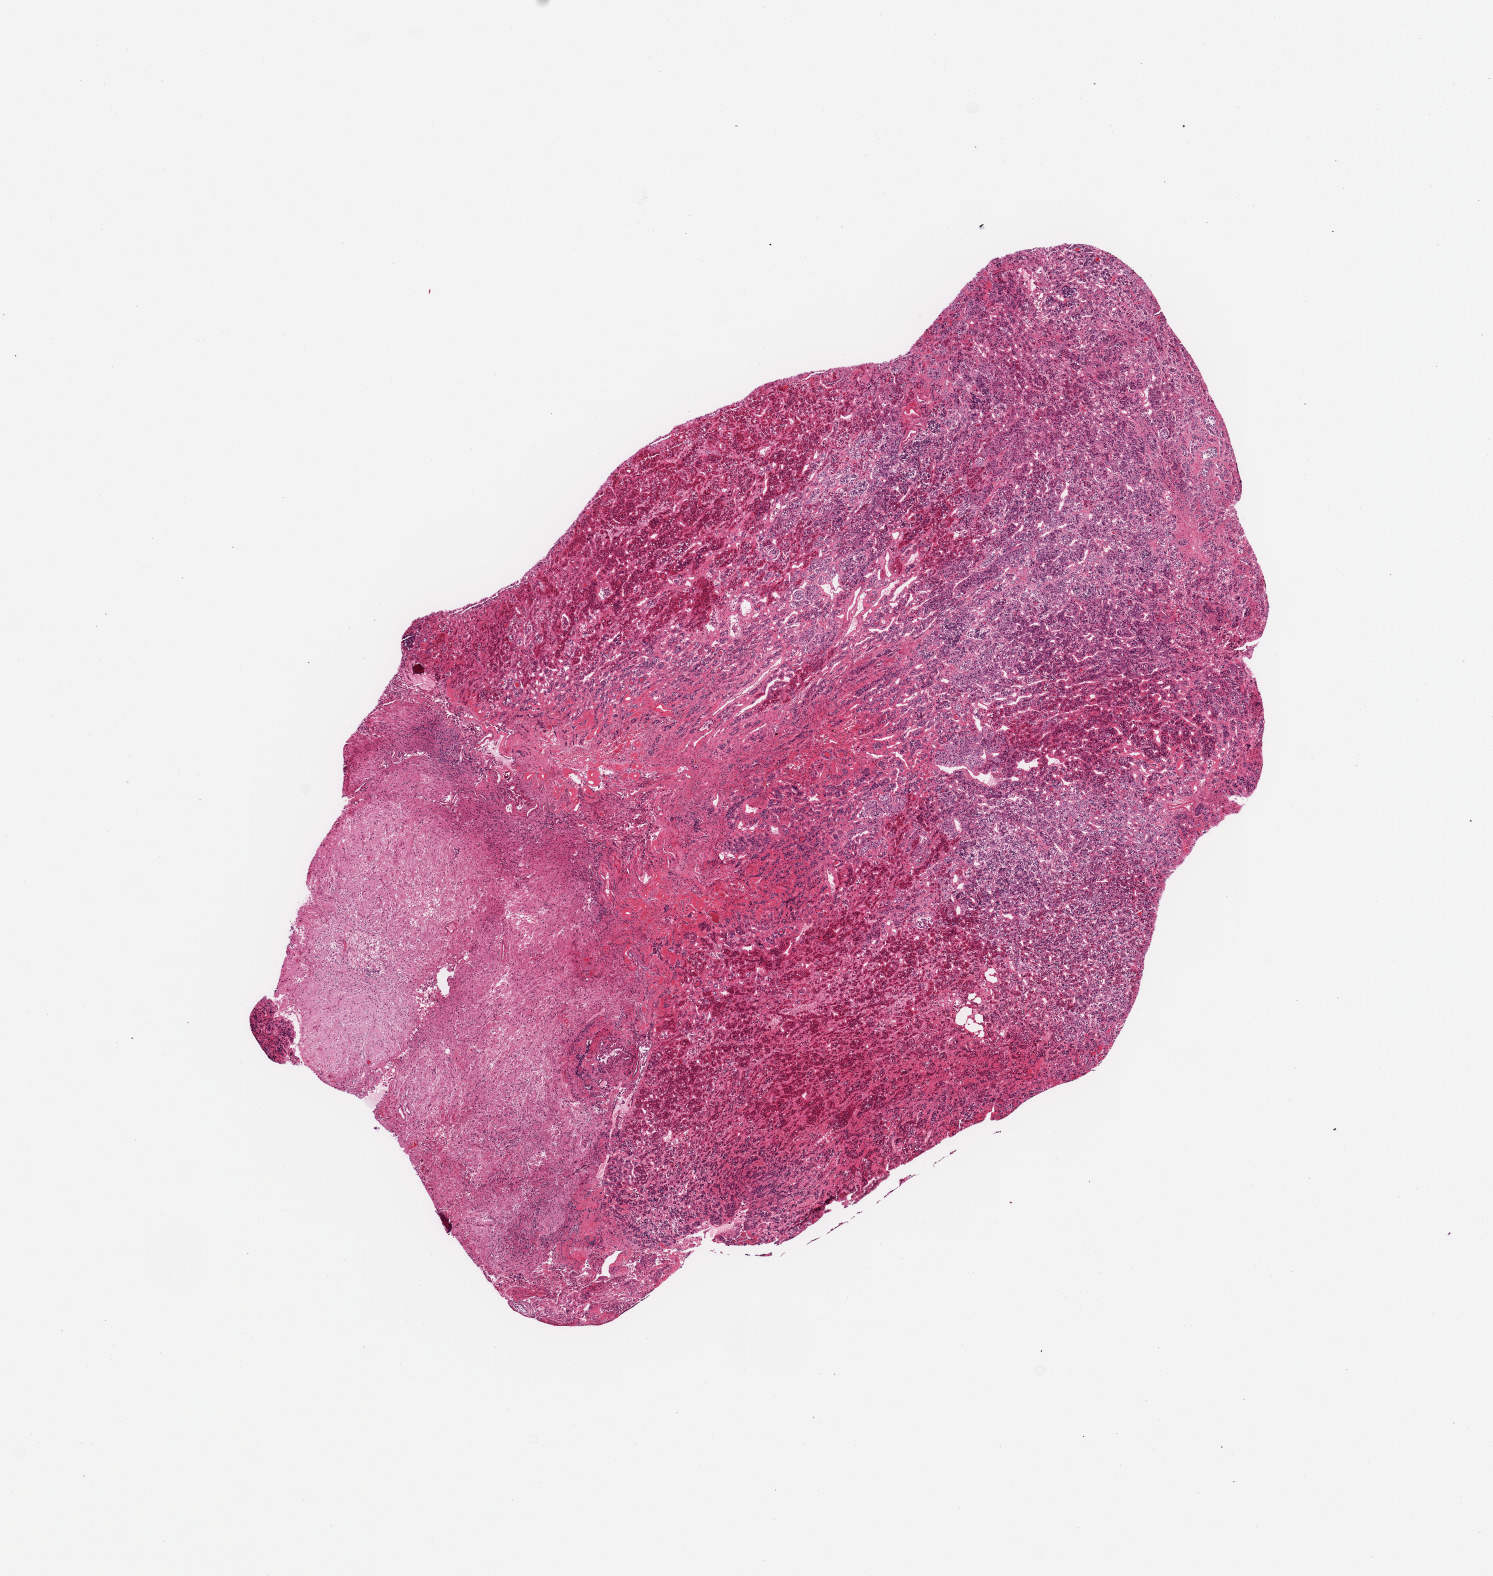
Digitized hematoxylin and eosin (H&E)-stained section, a low-resolution overview of the entire scanned area, about 11.8 x 12.5 mm (acquisition: 20x scan); PAXgene-fixed, paraffin-embedded tissue; sampled site (target tissue): pituitary; tissue donor sample.
• review note (as recorded): 1 piece: 70% adenohypophysis and 30% neurohypophysis